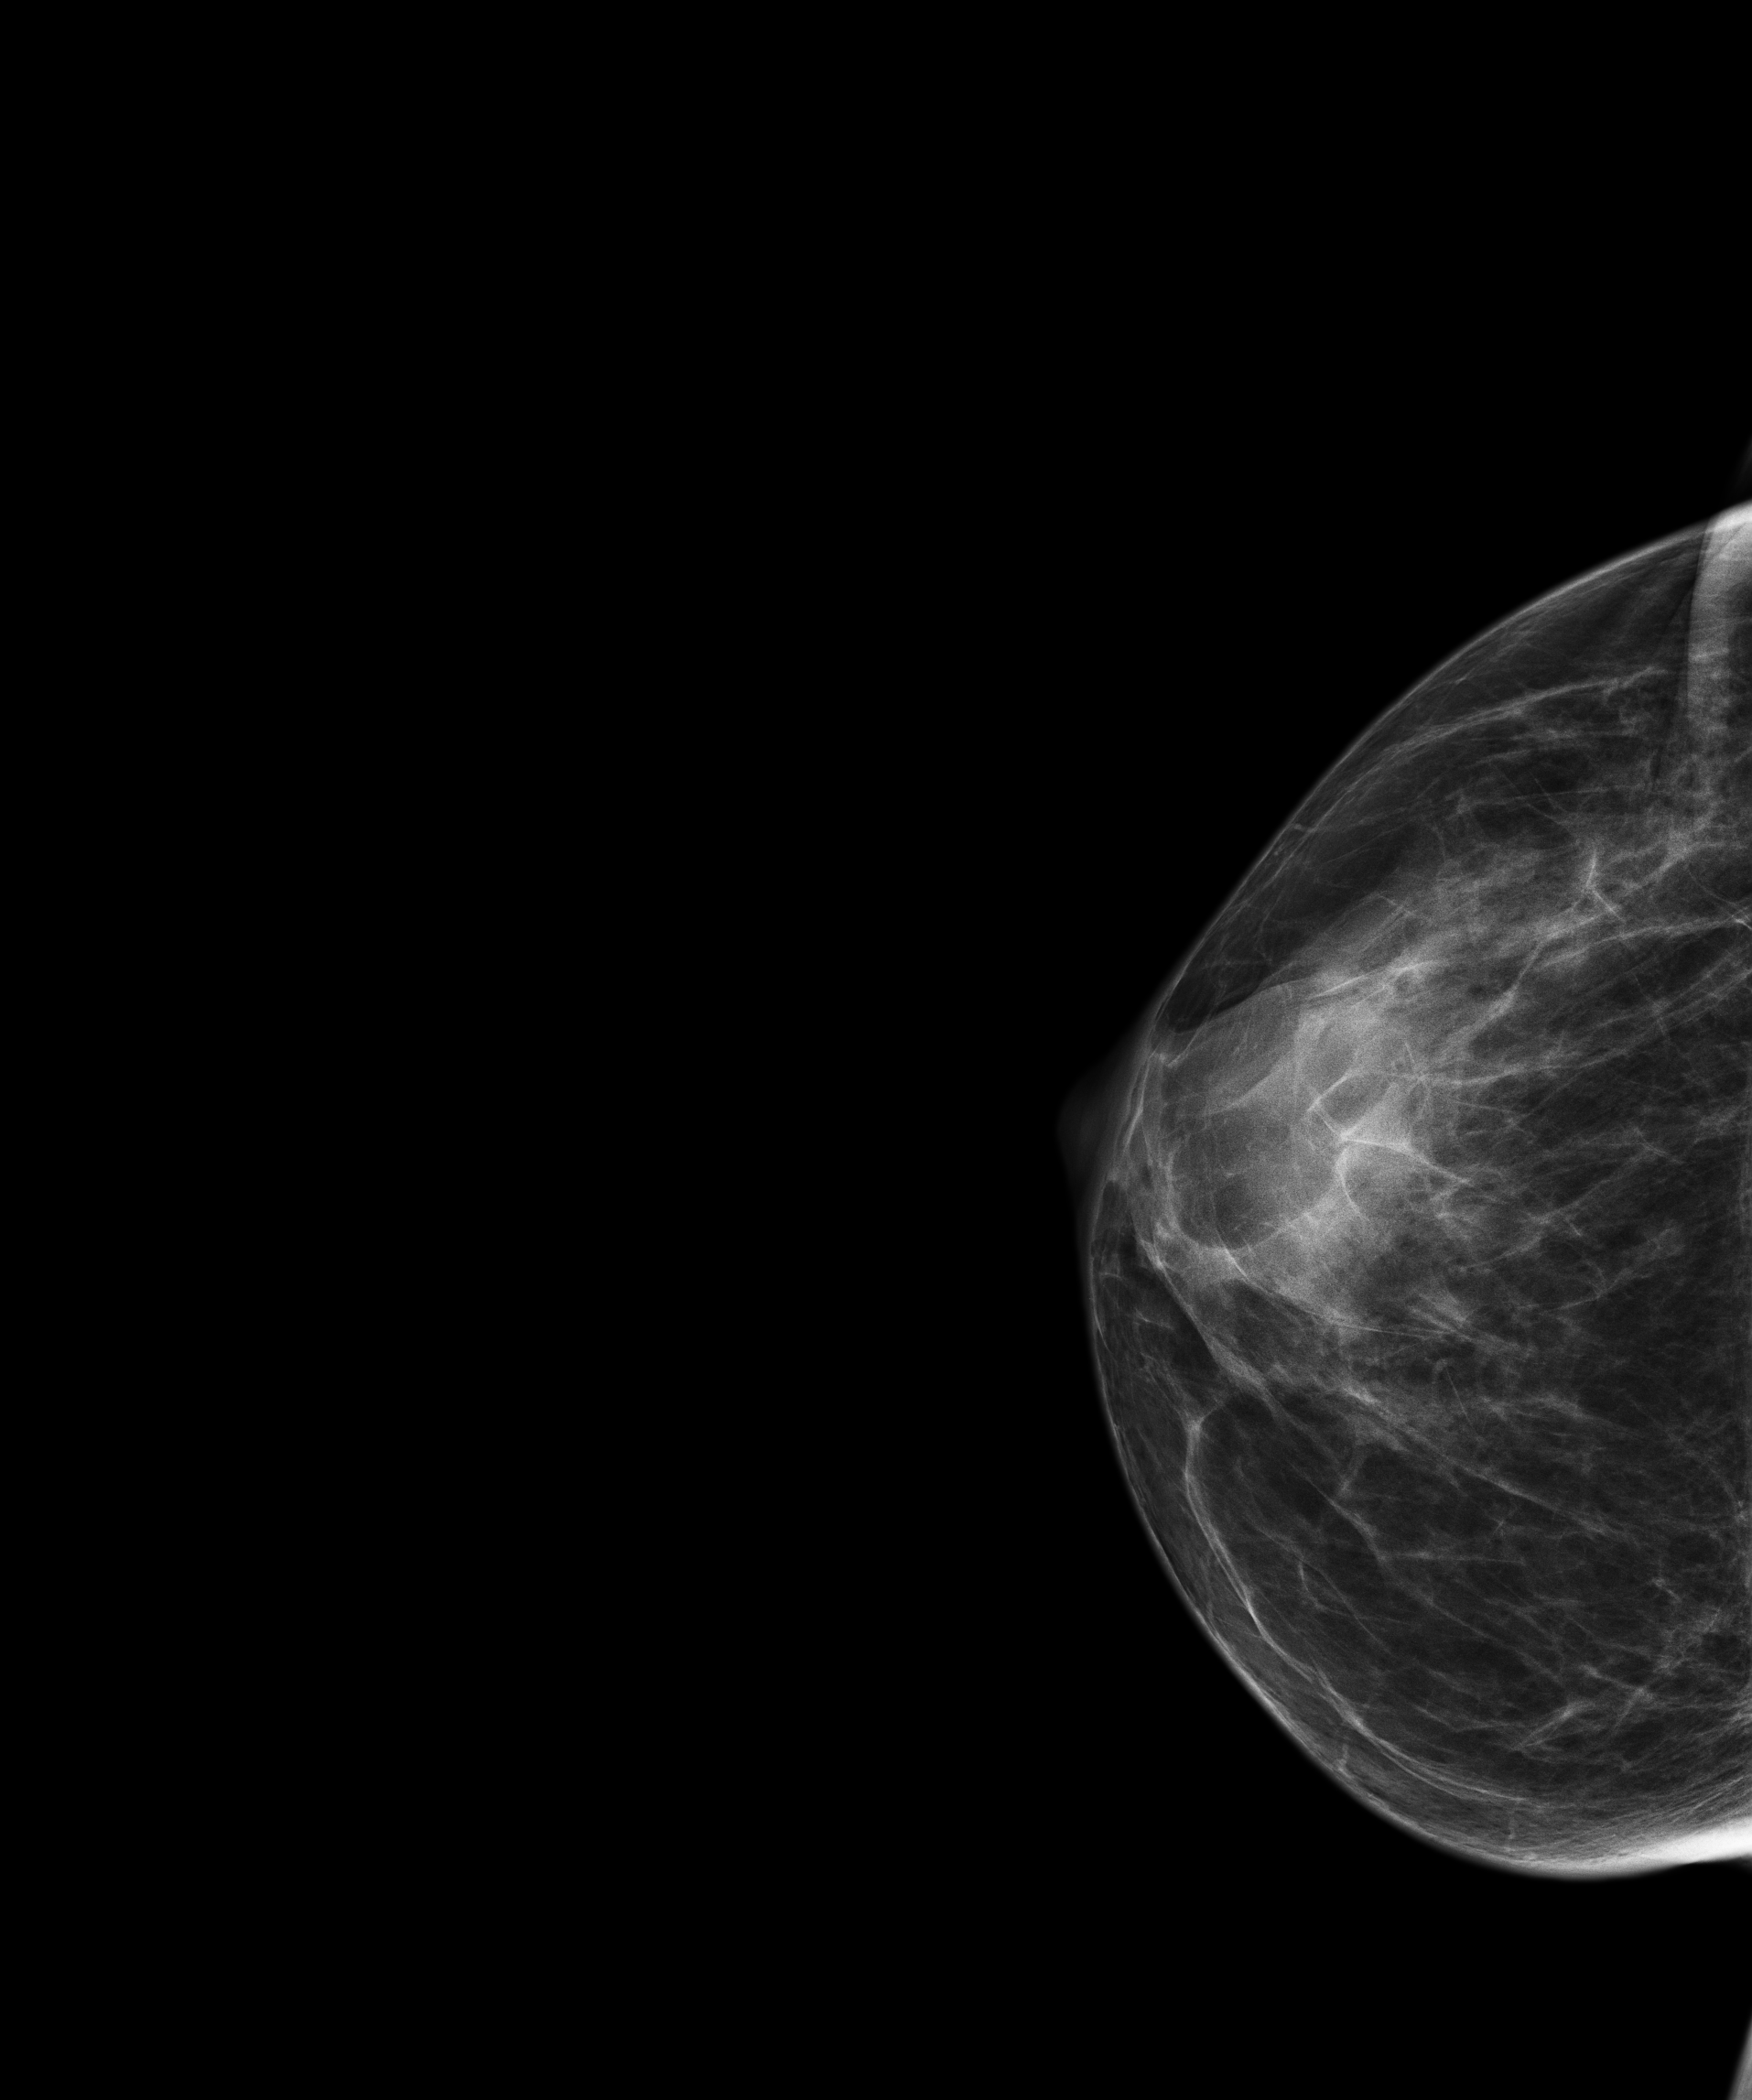
Full-field digital mammogram (FFDM), right breast, craniocaudal (CC) view, annual screening mammography examination, system: Senographe Essential ADS_56.21.3. Female patient, age 65 years.
- BI-RADS breast density category at the screening exam (both breasts, scale 1–4): 3
- final BI-RADS category for the screening round (tomosynthesis exam, both breasts): category 1
- recall: no recall after this screen